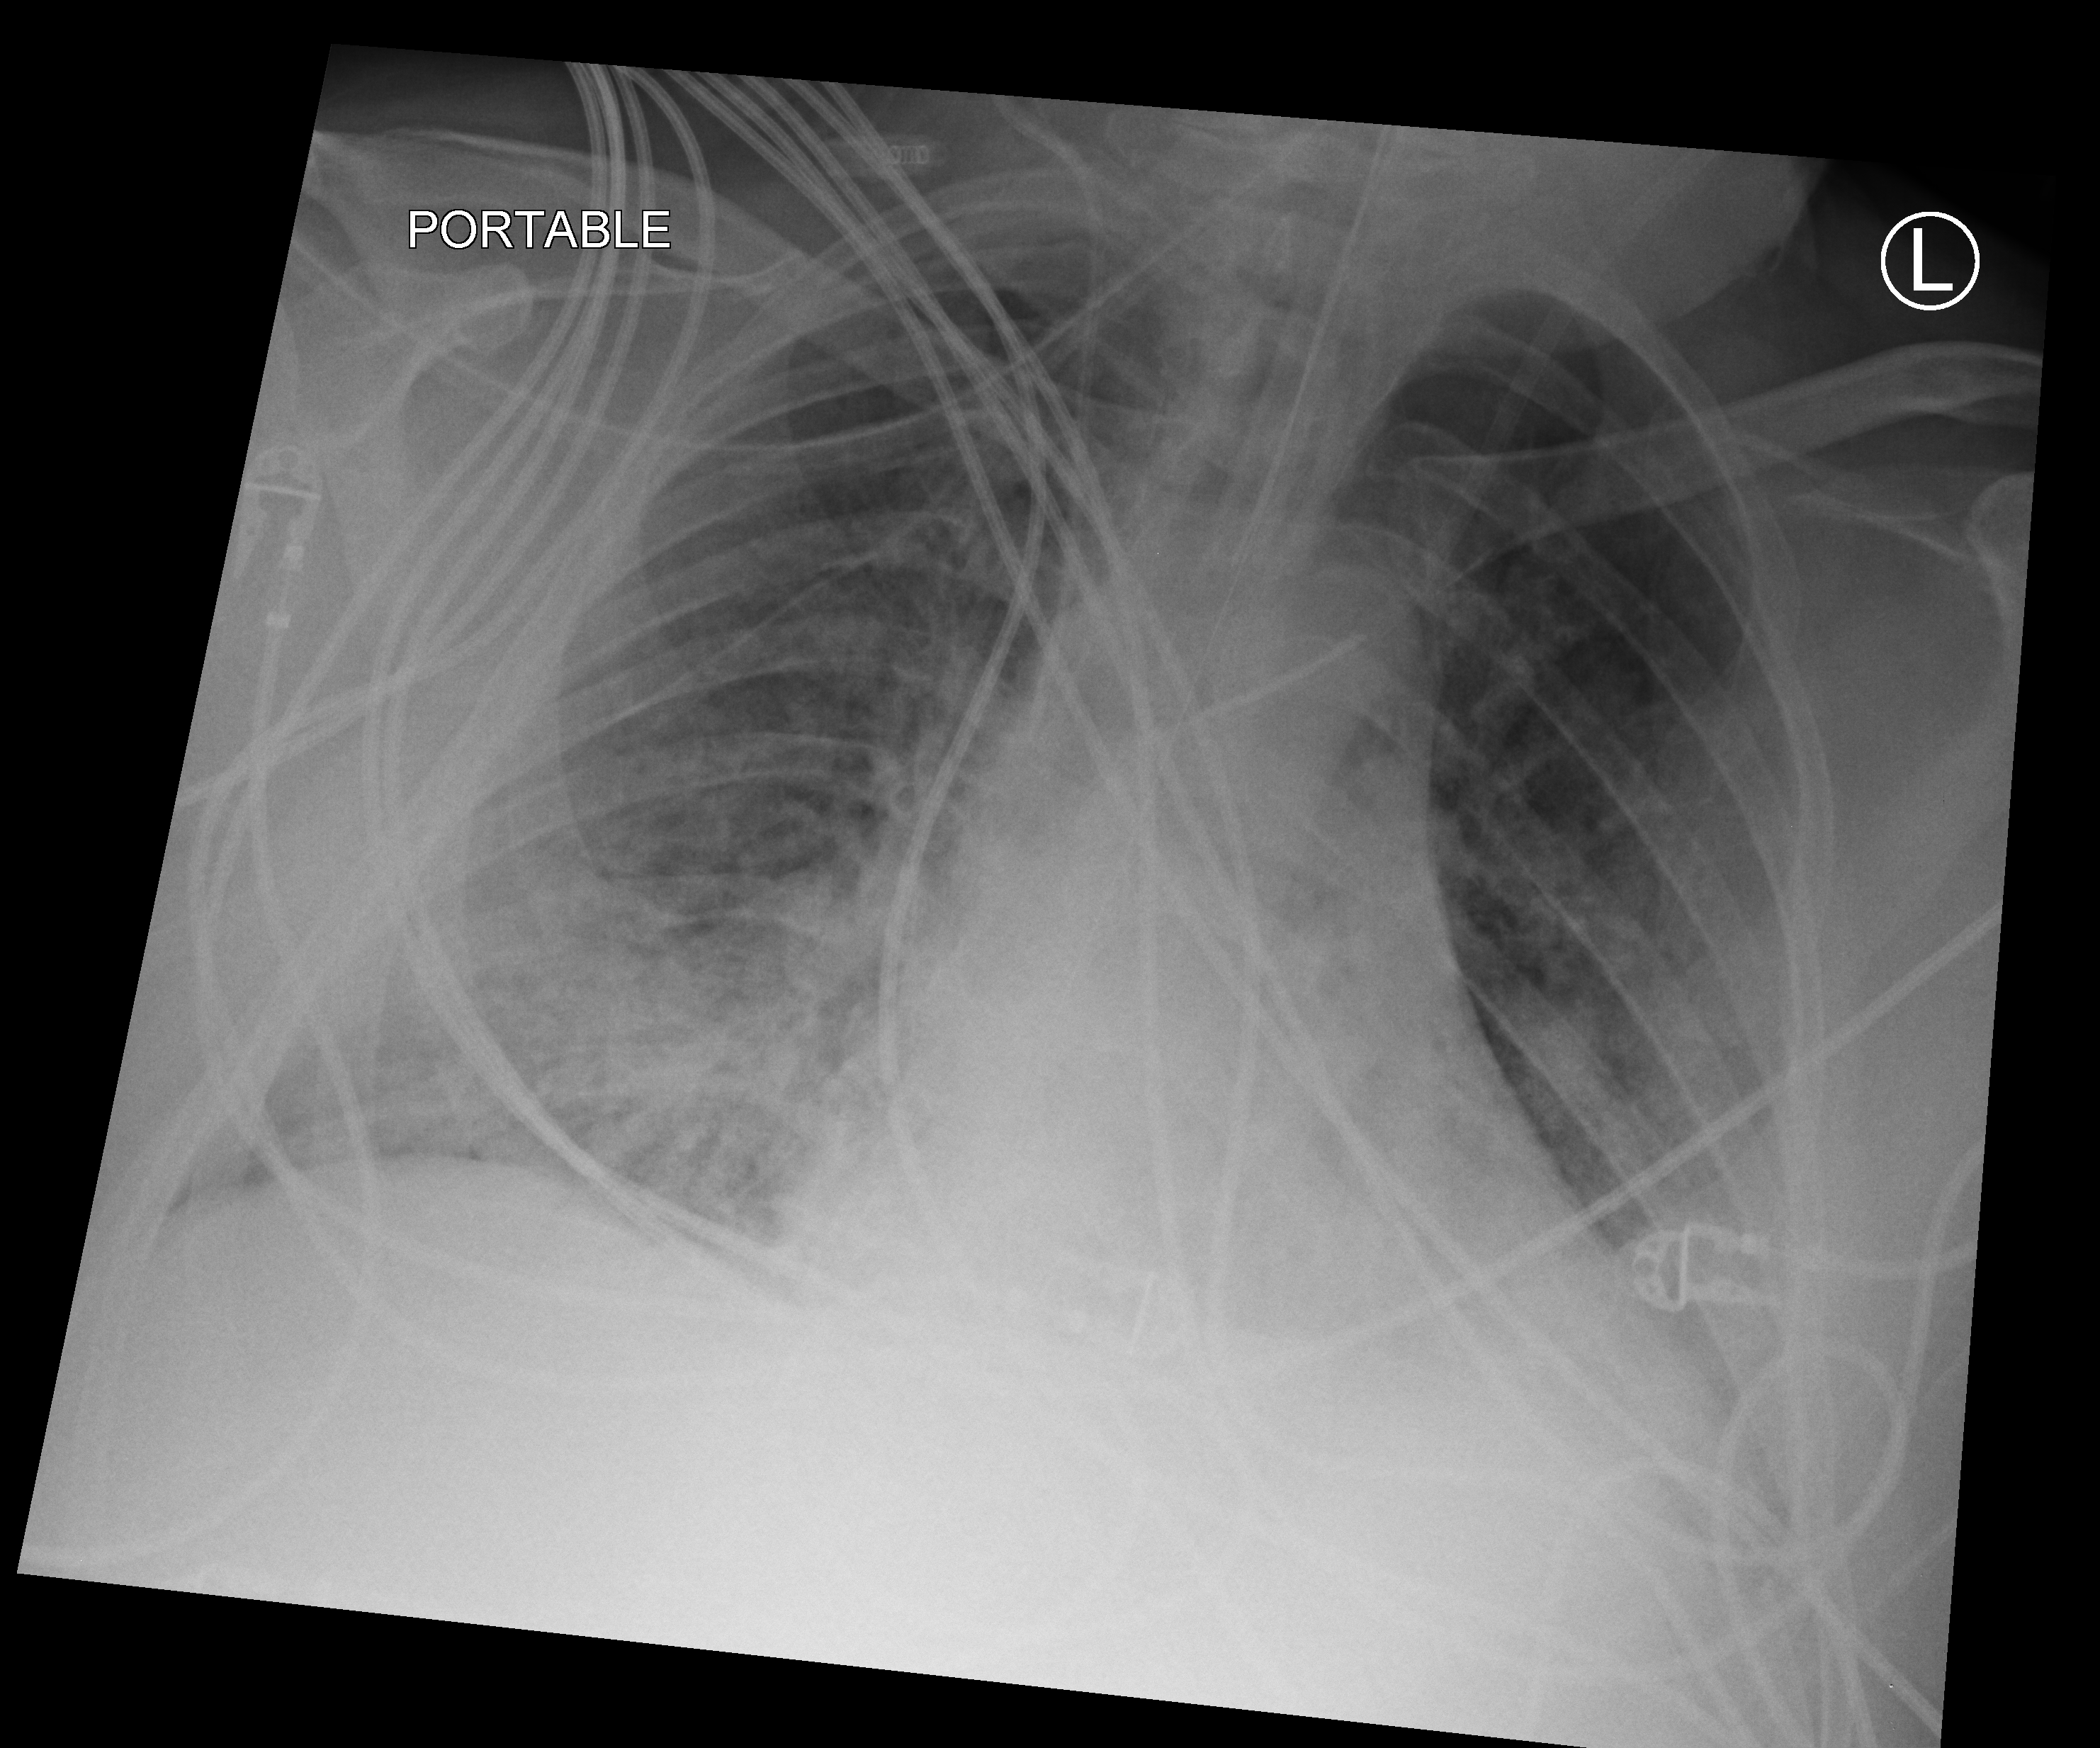
Bedside chest radiograph (computed radiography), anteroposterior (AP) projection. Male patient hospitalised with COVID-19, age 18–59 years.
Hospital-stay facts (about this admission, not read from this image; timing relative to this image not recorded): admitted to intensive care during this hospital stay: yes.